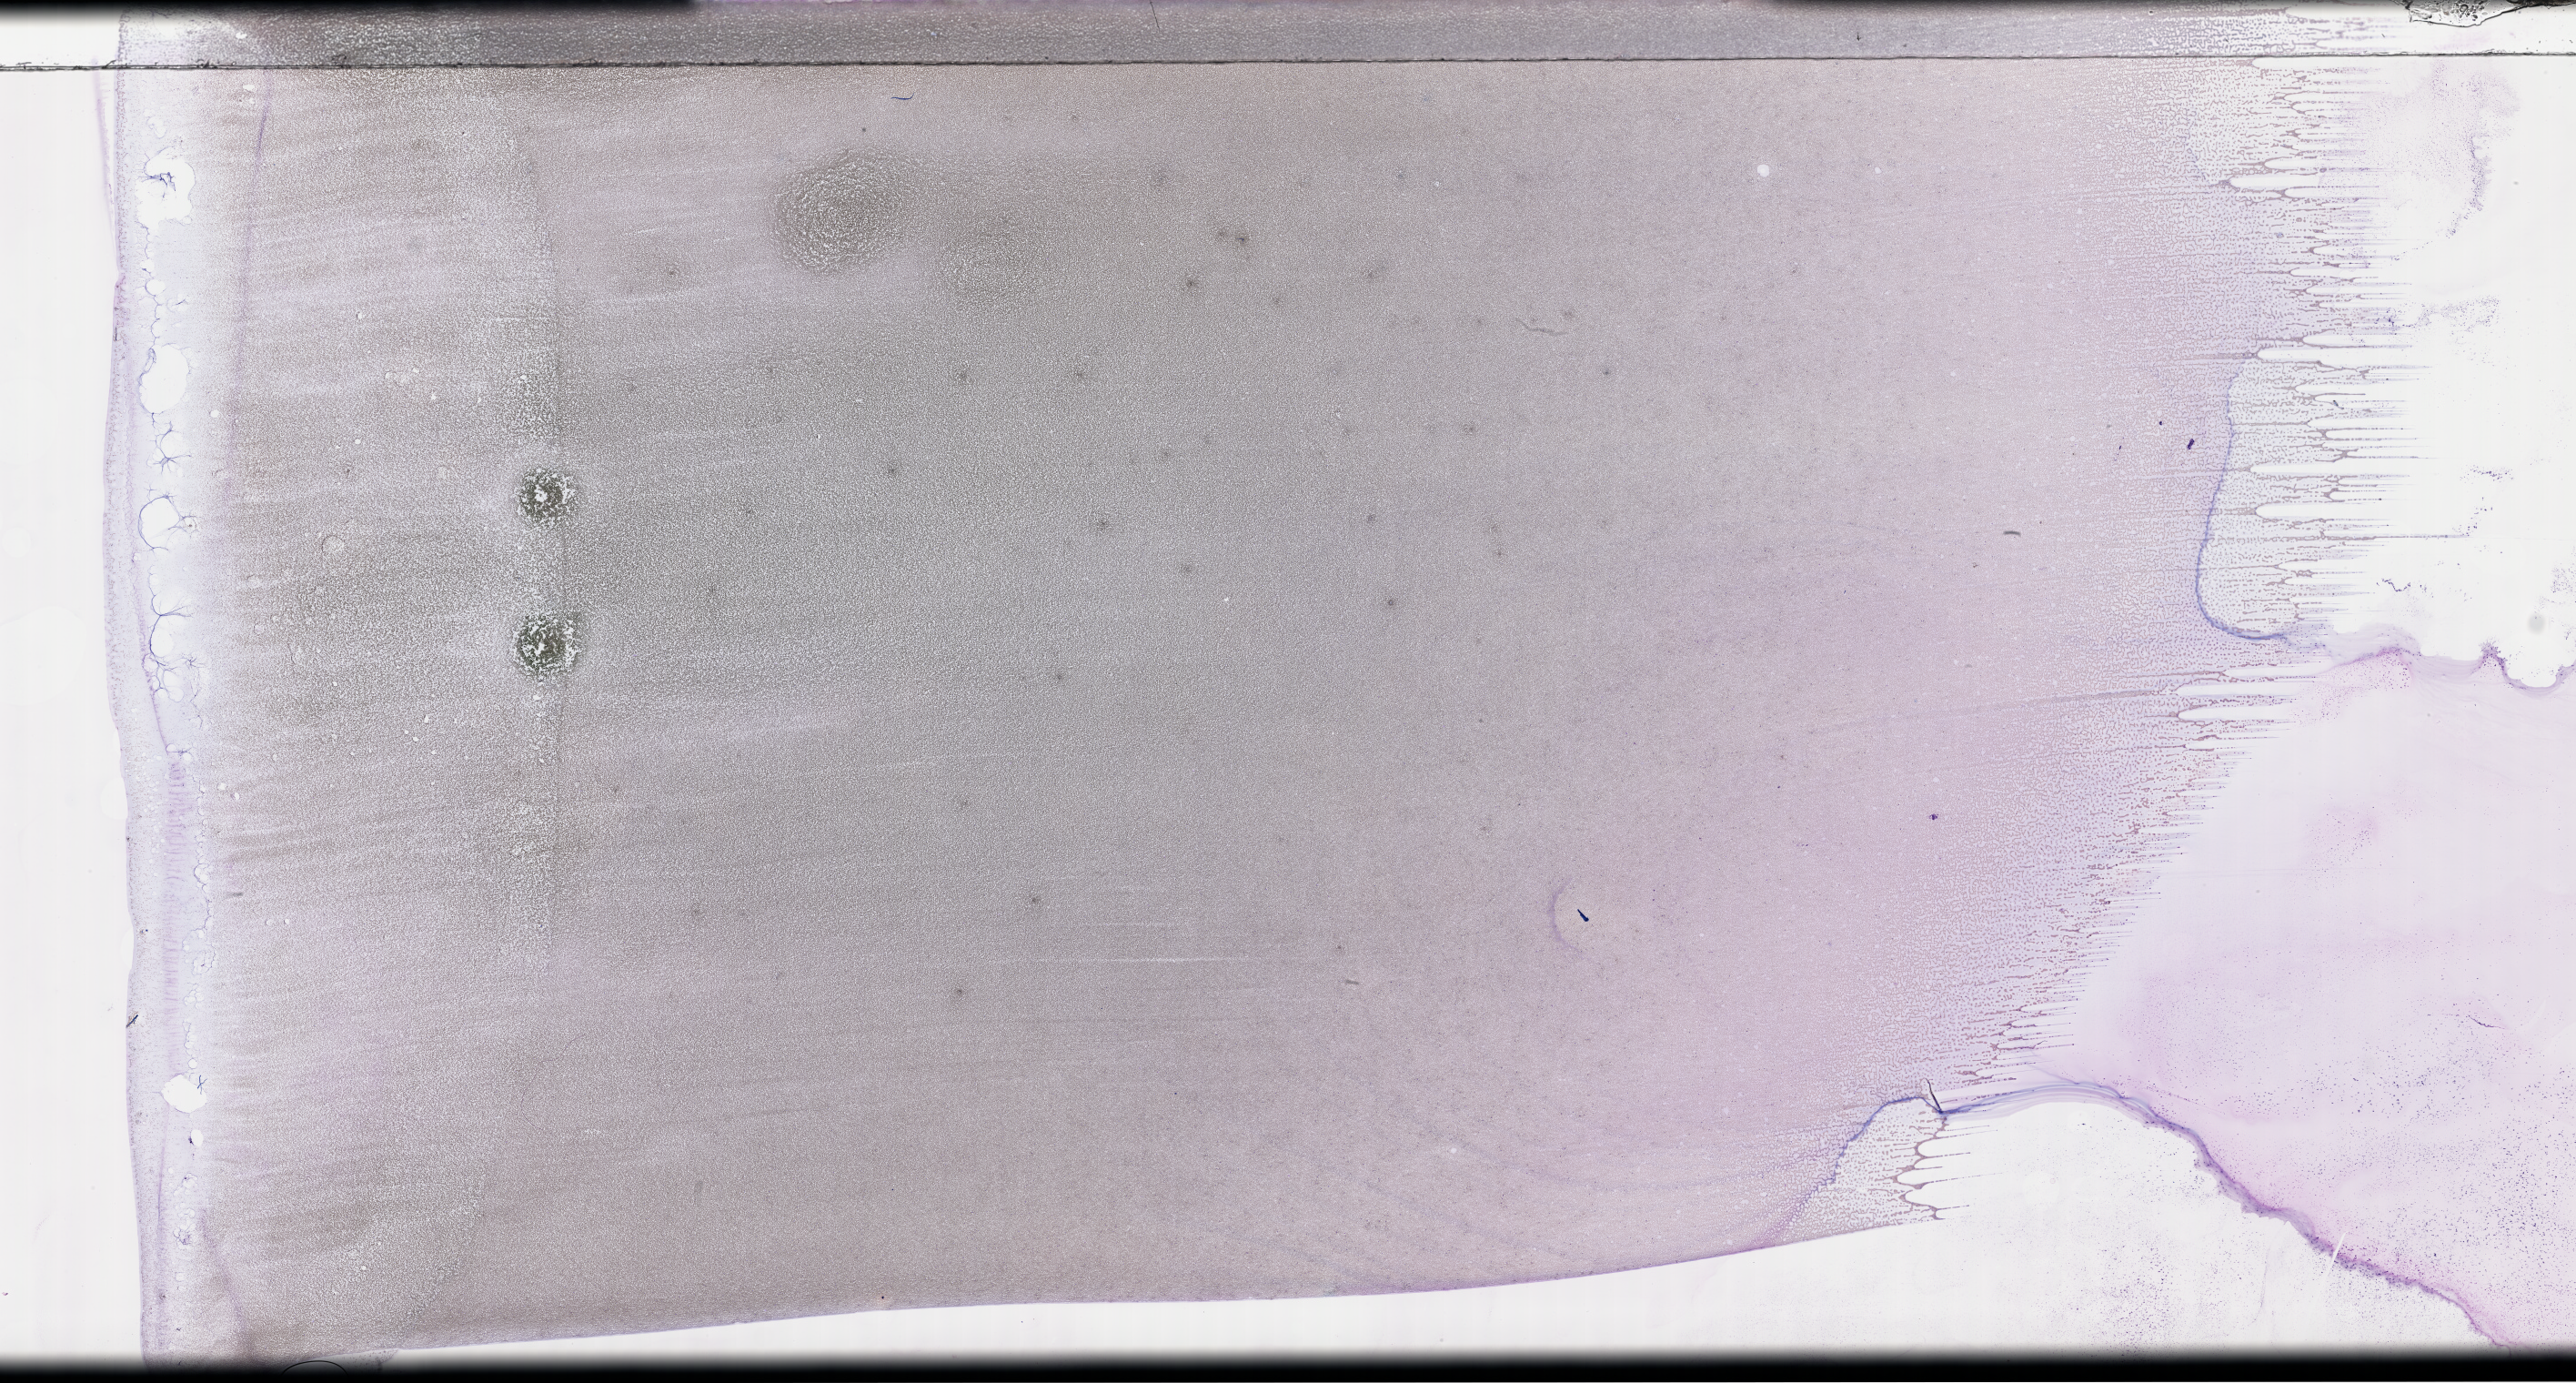
Whole-slide image of a whole blood smear, Wright–Giemsa stain — a low-resolution overview of the entire scanned area, about 45.7 x 24.5 mm. Smear from an EDTA sample. Specimen time point: collected on treatment. Patient: female.
Patient diagnosis: Plasma Cell Myeloma.